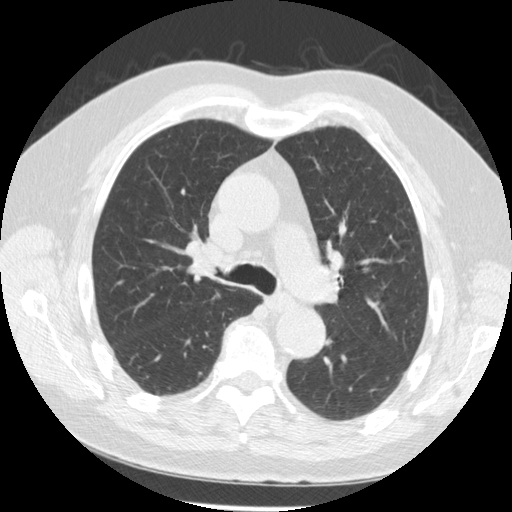
Low-dose screening chest CT, one axial slice; reconstruction kernel STANDARD; lung window (W 1500 / L -600 HU); 2.5 mm slice thickness; 512 × 512 image matrix, field of view 355 × 355 mm.
Outlined on this slice (expert manual segmentation):
- lesion 2 (tumor, hilum of right lung): bounding box <187,245,217,276> (left, top, right, bottom; pixels)